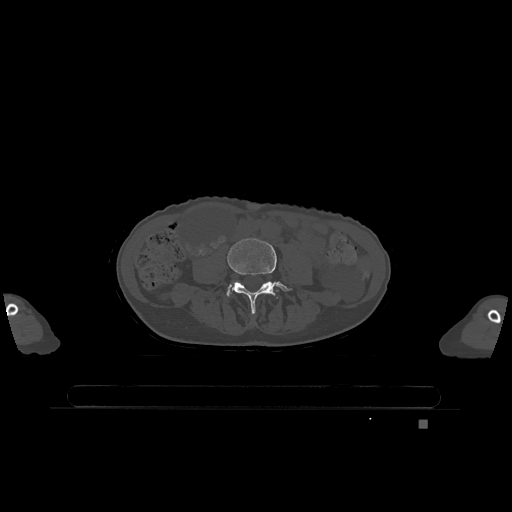
CT including the spine, one axial slice. Position 294 of 1317 along the scan axis. Bone window (W 1800 / L 400 HU). 512 × 512 image matrix, field of view 500 × 500 mm. Female patient, age 74 years. From the clinical record (not read from this slice): primary cancer: lung; vertebrae with lytic lesions (as recorded): T1, T4, T5, T6, L4, L5.
Annotated regions visible in this slice (semi-automatically segmented with operator editing):
- L4 vertebra: box from (x=227, y=238) to (x=292, y=313) px
- L5 vertebra: (x=228, y=290)–(x=230, y=293)